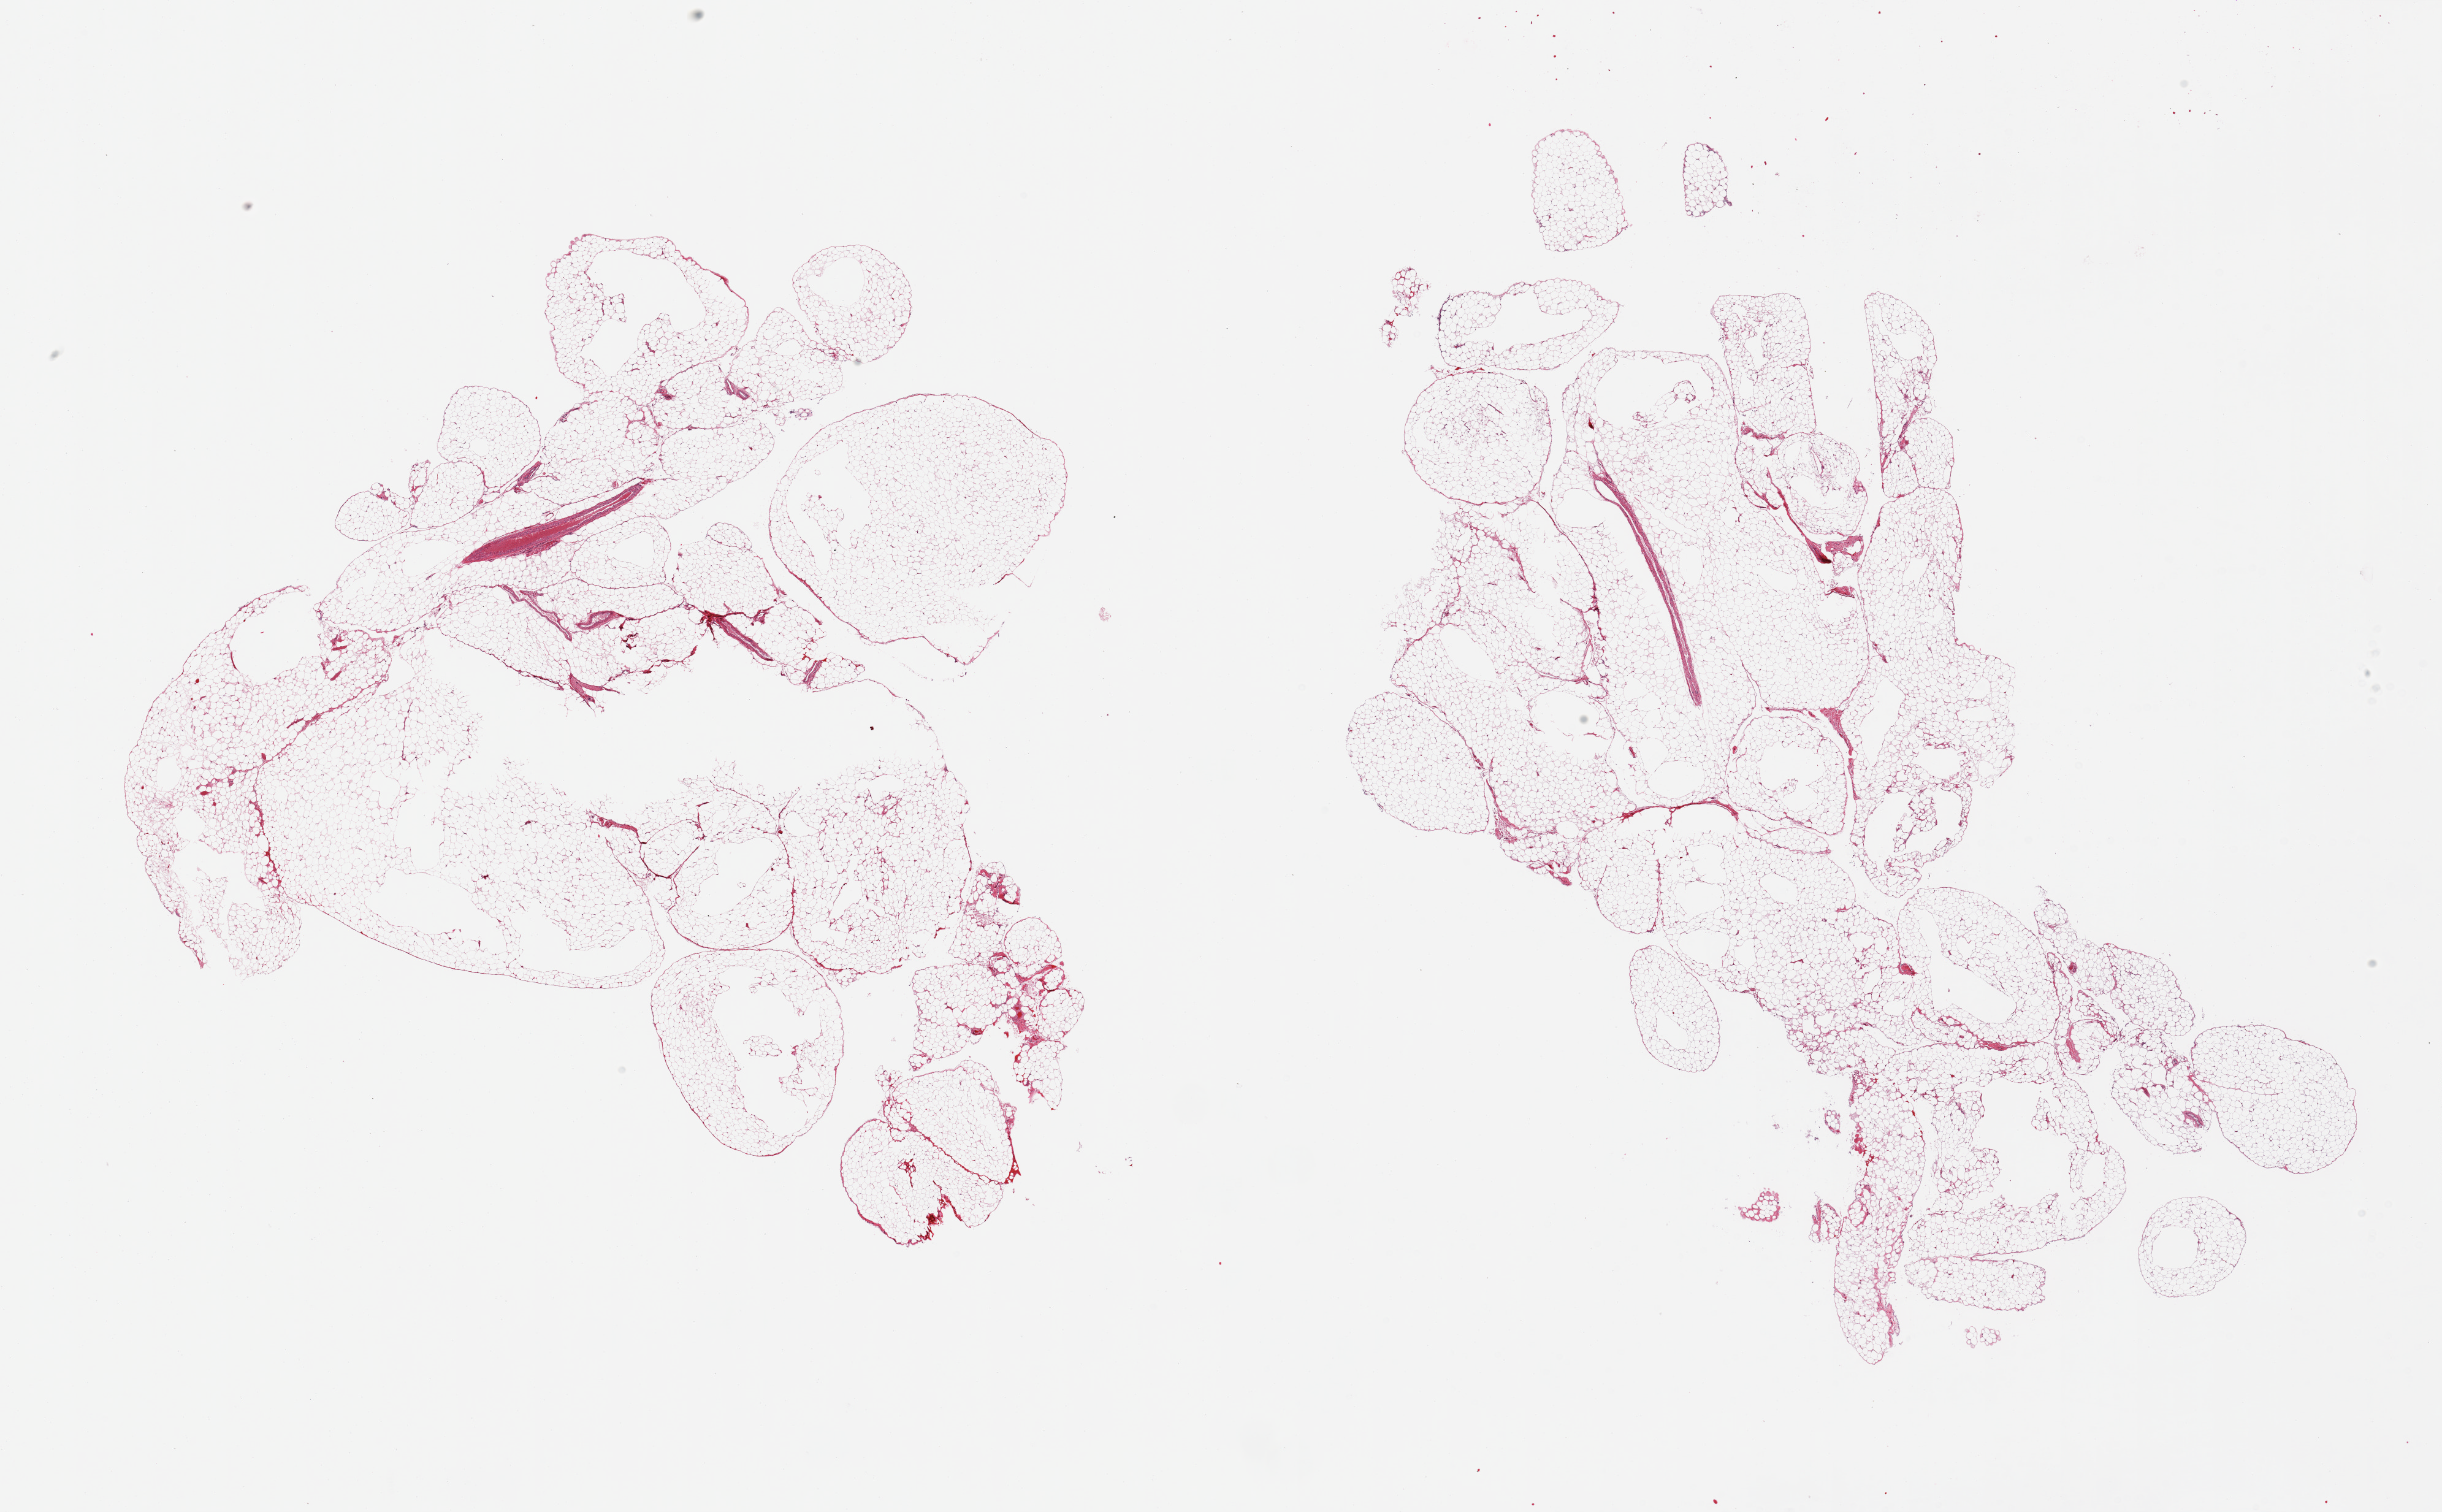
Digitized hematoxylin and eosin (H&E)-stained section — a low-resolution overview of the entire scanned area, about 31.5 x 19.5 mm (from a 20x scan). PAXgene-fixed paraffin-embedded (PFPE) section. Target tissue: omentum. Donor tissue sample. Donor: female.
Review note (as recorded): 2 pieces.